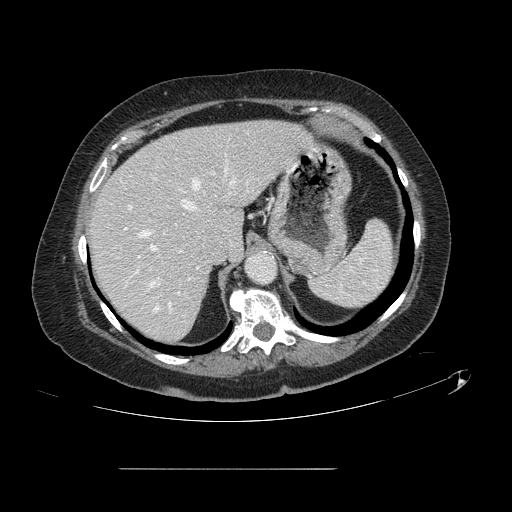
Contrast-enhanced abdominal CT, one axial slice. Slice 100 of 148 in the series (ordered by position). Intravenous contrast given. Soft-tissue window (W 400 / L 40 HU). 2.5 mm slice thickness. 512 × 512 image matrix. Female patient, age 75 years. From the clinical record (not read from this slice): diagnosis: colorectal cancer liver metastases, imaged before liver resection; multiple liver metastases: no; largest metastasis: 2.4 cm; chemotherapy before resection: no.
Outlined on this slice (manually delineated by an expert):
- hepatic veins: box from (x=140, y=168) to (x=248, y=311) px
- liver: (x=89, y=120)–(x=308, y=342)
- planned liver remnant (the part of the liver to remain after resection): (x=90, y=120)–(x=309, y=342)
- portal vein (with intrahepatic branches): (x=129, y=178)–(x=179, y=294)